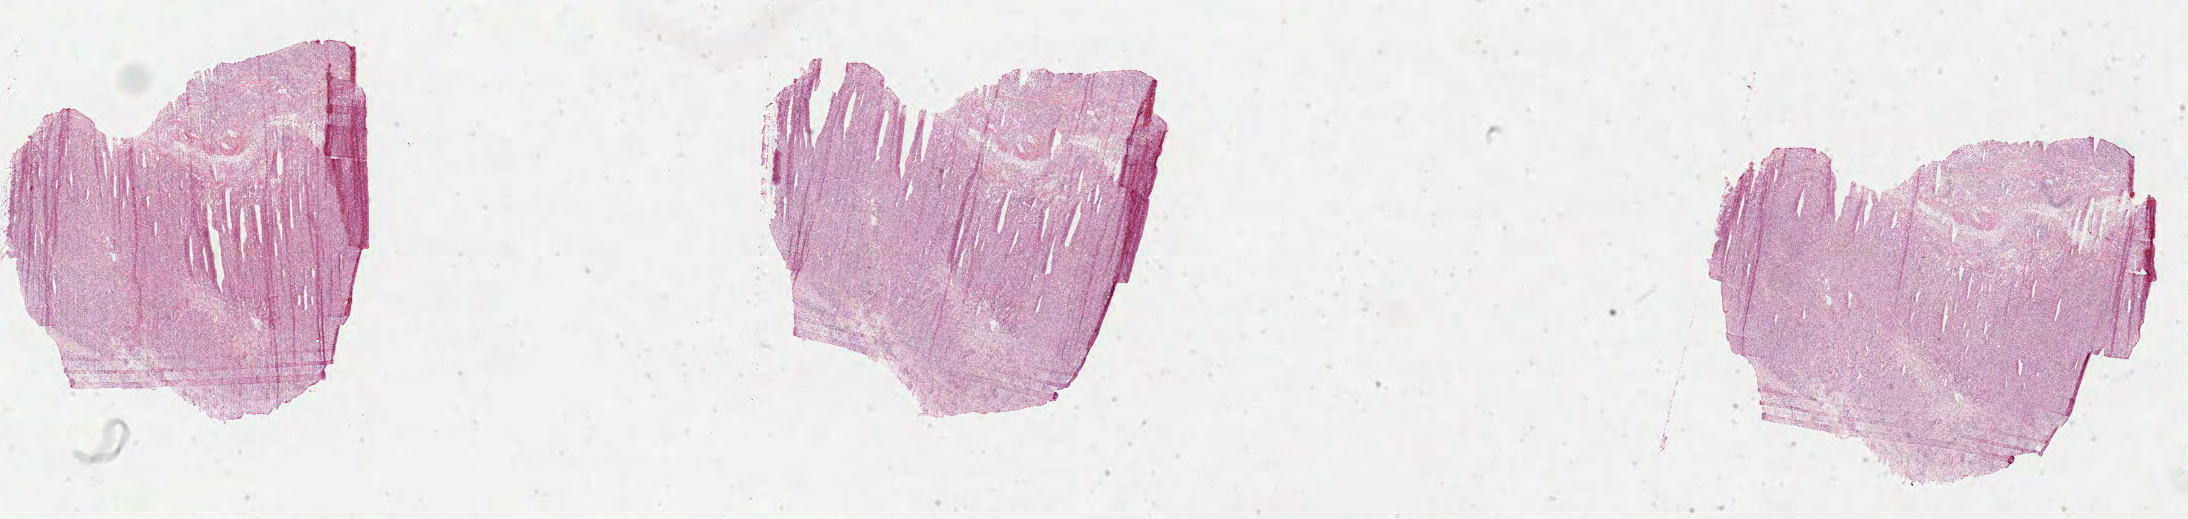
H&E-stained whole-slide image — a low-resolution overview of the entire scanned area, about 35.3 x 8.4 mm, formalin-fixed paraffin-embedded (FFPE) diagnostic section, primary tumour sample from the stomach. Patient: male, age at initial diagnosis 53 years. Histologic grade: G3 (poorly differentiated).
* lymph nodes positive (case pathology): 11 of 22 examined
* AJCC pathologic stage: IIIA (7th edition)
* pathologic diagnosis: Carcinoma, diffuse type (body of stomach)